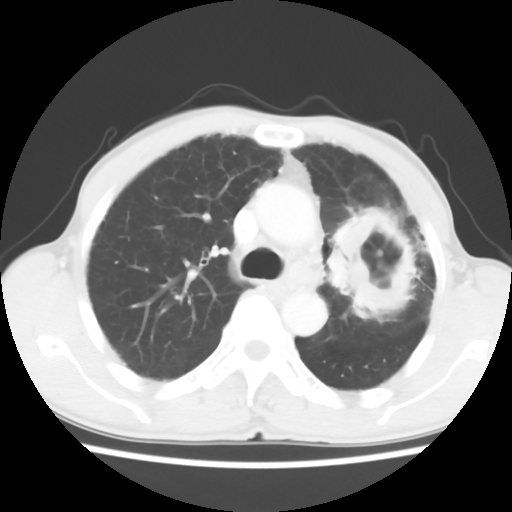
Chest CT, one axial slice; 120 kVp; lung window (W 1500 / L -600 HU); 5 mm slice thickness; 512 × 512 image matrix, field of view 308 × 308 mm. Male patient, age 64 years. Case-level facts recorded for this patient, not image findings: clinical TNM (as recorded): T3 N3 M0; histopathological grade: G3.
Structures marked on this image (rectangle marked by the reading radiologist):
- lung tumour (recorded histology: adenocarcinoma): bounding box (x1, y1, x2, y2) in pixels: (325, 194, 432, 332)